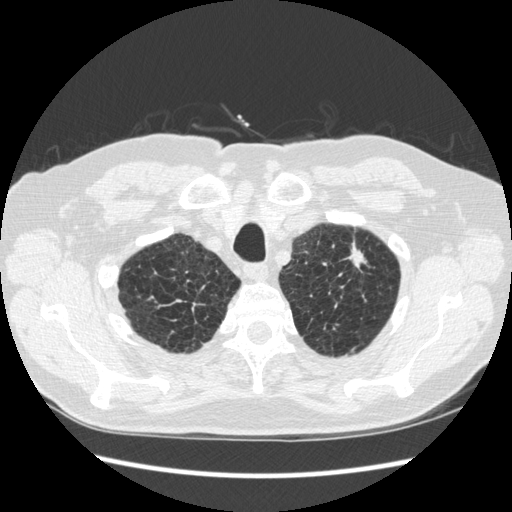
Low-dose screening chest CT, one axial slice. Slice 235 of 267 in the series (ordered by position). Reconstruction kernel STANDARD. Lung window (W 1500 / L -600 HU). 512 × 512 image matrix, field of view 360 × 360 mm.
Structures marked on this image (outlined manually by an expert reader):
- lesion 1 (tumor, upper lobe of left lung): bounding box <349,242,366,268> (left, top, right, bottom; pixels)